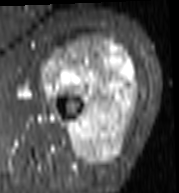
MRI of an extremity soft-tissue mass, one axial slice; position 68 of 103 along the scan axis; STIR; MR volume resampled by the dataset authors to the PET/CT grid (not the native acquisition matrix); 3.27 mm slice thickness; 179 × 193 image matrix, field of view 175 × 188 mm. Female patient. From the clinical record (not read from this slice): histological type: undifferentiated – high grade; grade: high; site of the primary tumour: left thigh.
Outlined on this slice (expert contour drawn on MRI and transferred to this co-registered scan by the dataset authors):
- gross tumour volume including surrounding oedema: bounding box <43,35,140,166> (left, top, right, bottom; pixels)
- gross tumour volume (mass): <43,35,138,166>